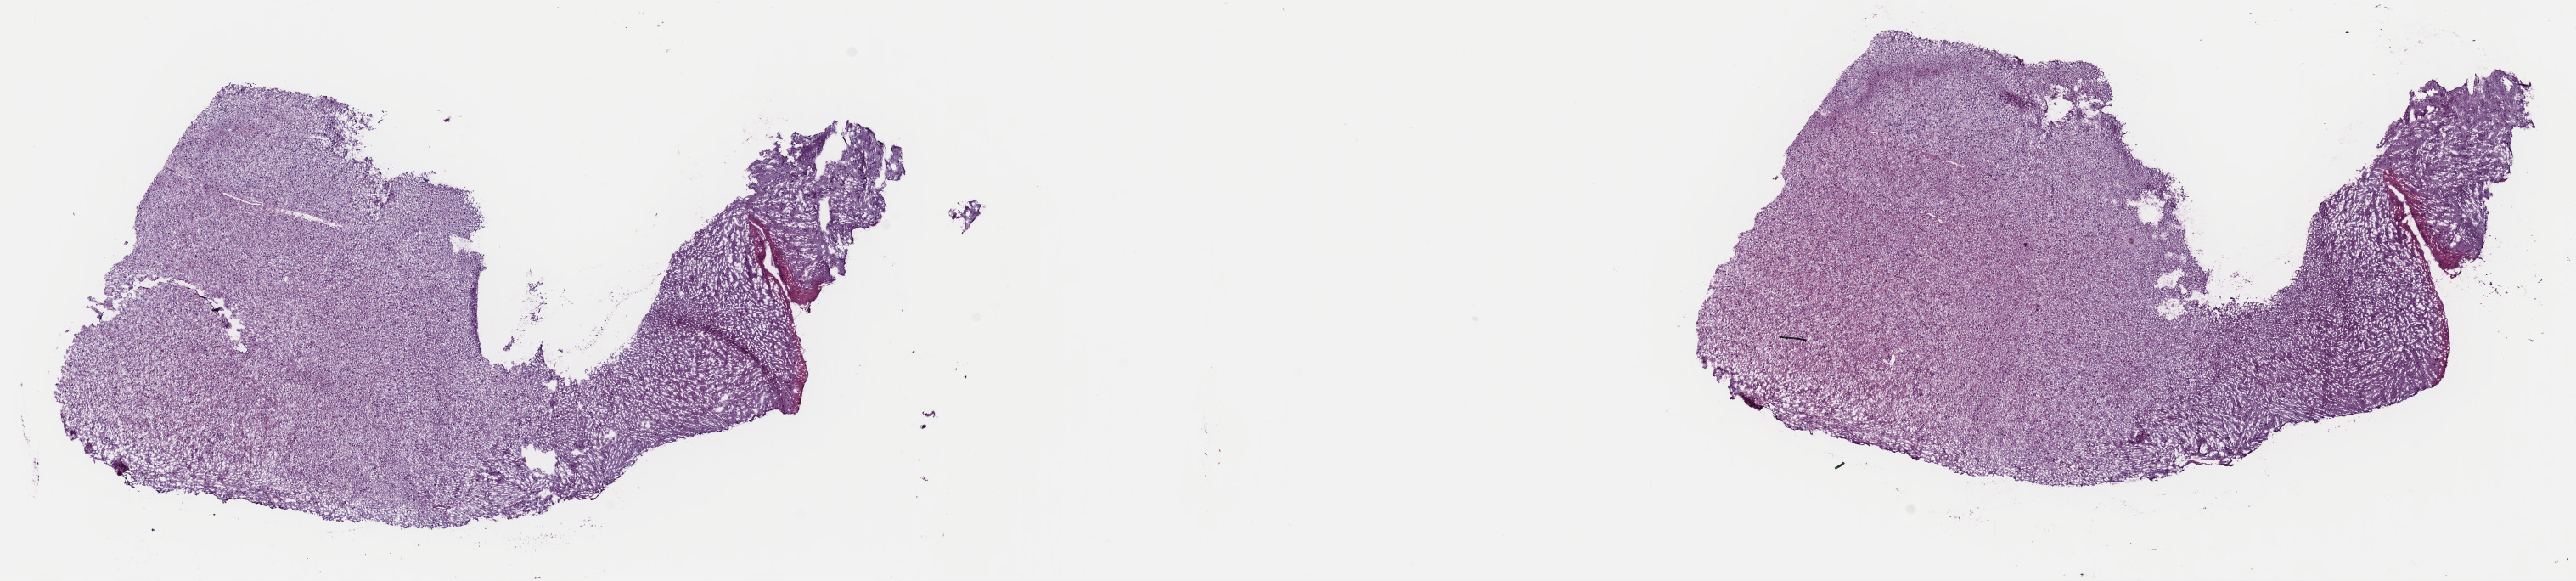
Digitized H&E-stained tissue section (whole slide), low-resolution overview of the scanned area, about 24.0 x 5.4 mm (slide scanned at 40x); frozen section; sample: primary tumour, brain. Patient: female, age at initial diagnosis 33 years. Histologic grade: G2 (moderately differentiated). Composition of this section per pathologist review: tumour cells 50%, tumour nuclei 75%, normal cells 10%, stromal cells 40%, necrosis 0%. Inflammatory infiltration, as recorded: lymphocyte infiltration 0%, monocyte infiltration 0%, neutrophil infiltration 0%.
Pathologic diagnosis: Oligodendroglioma, NOS.